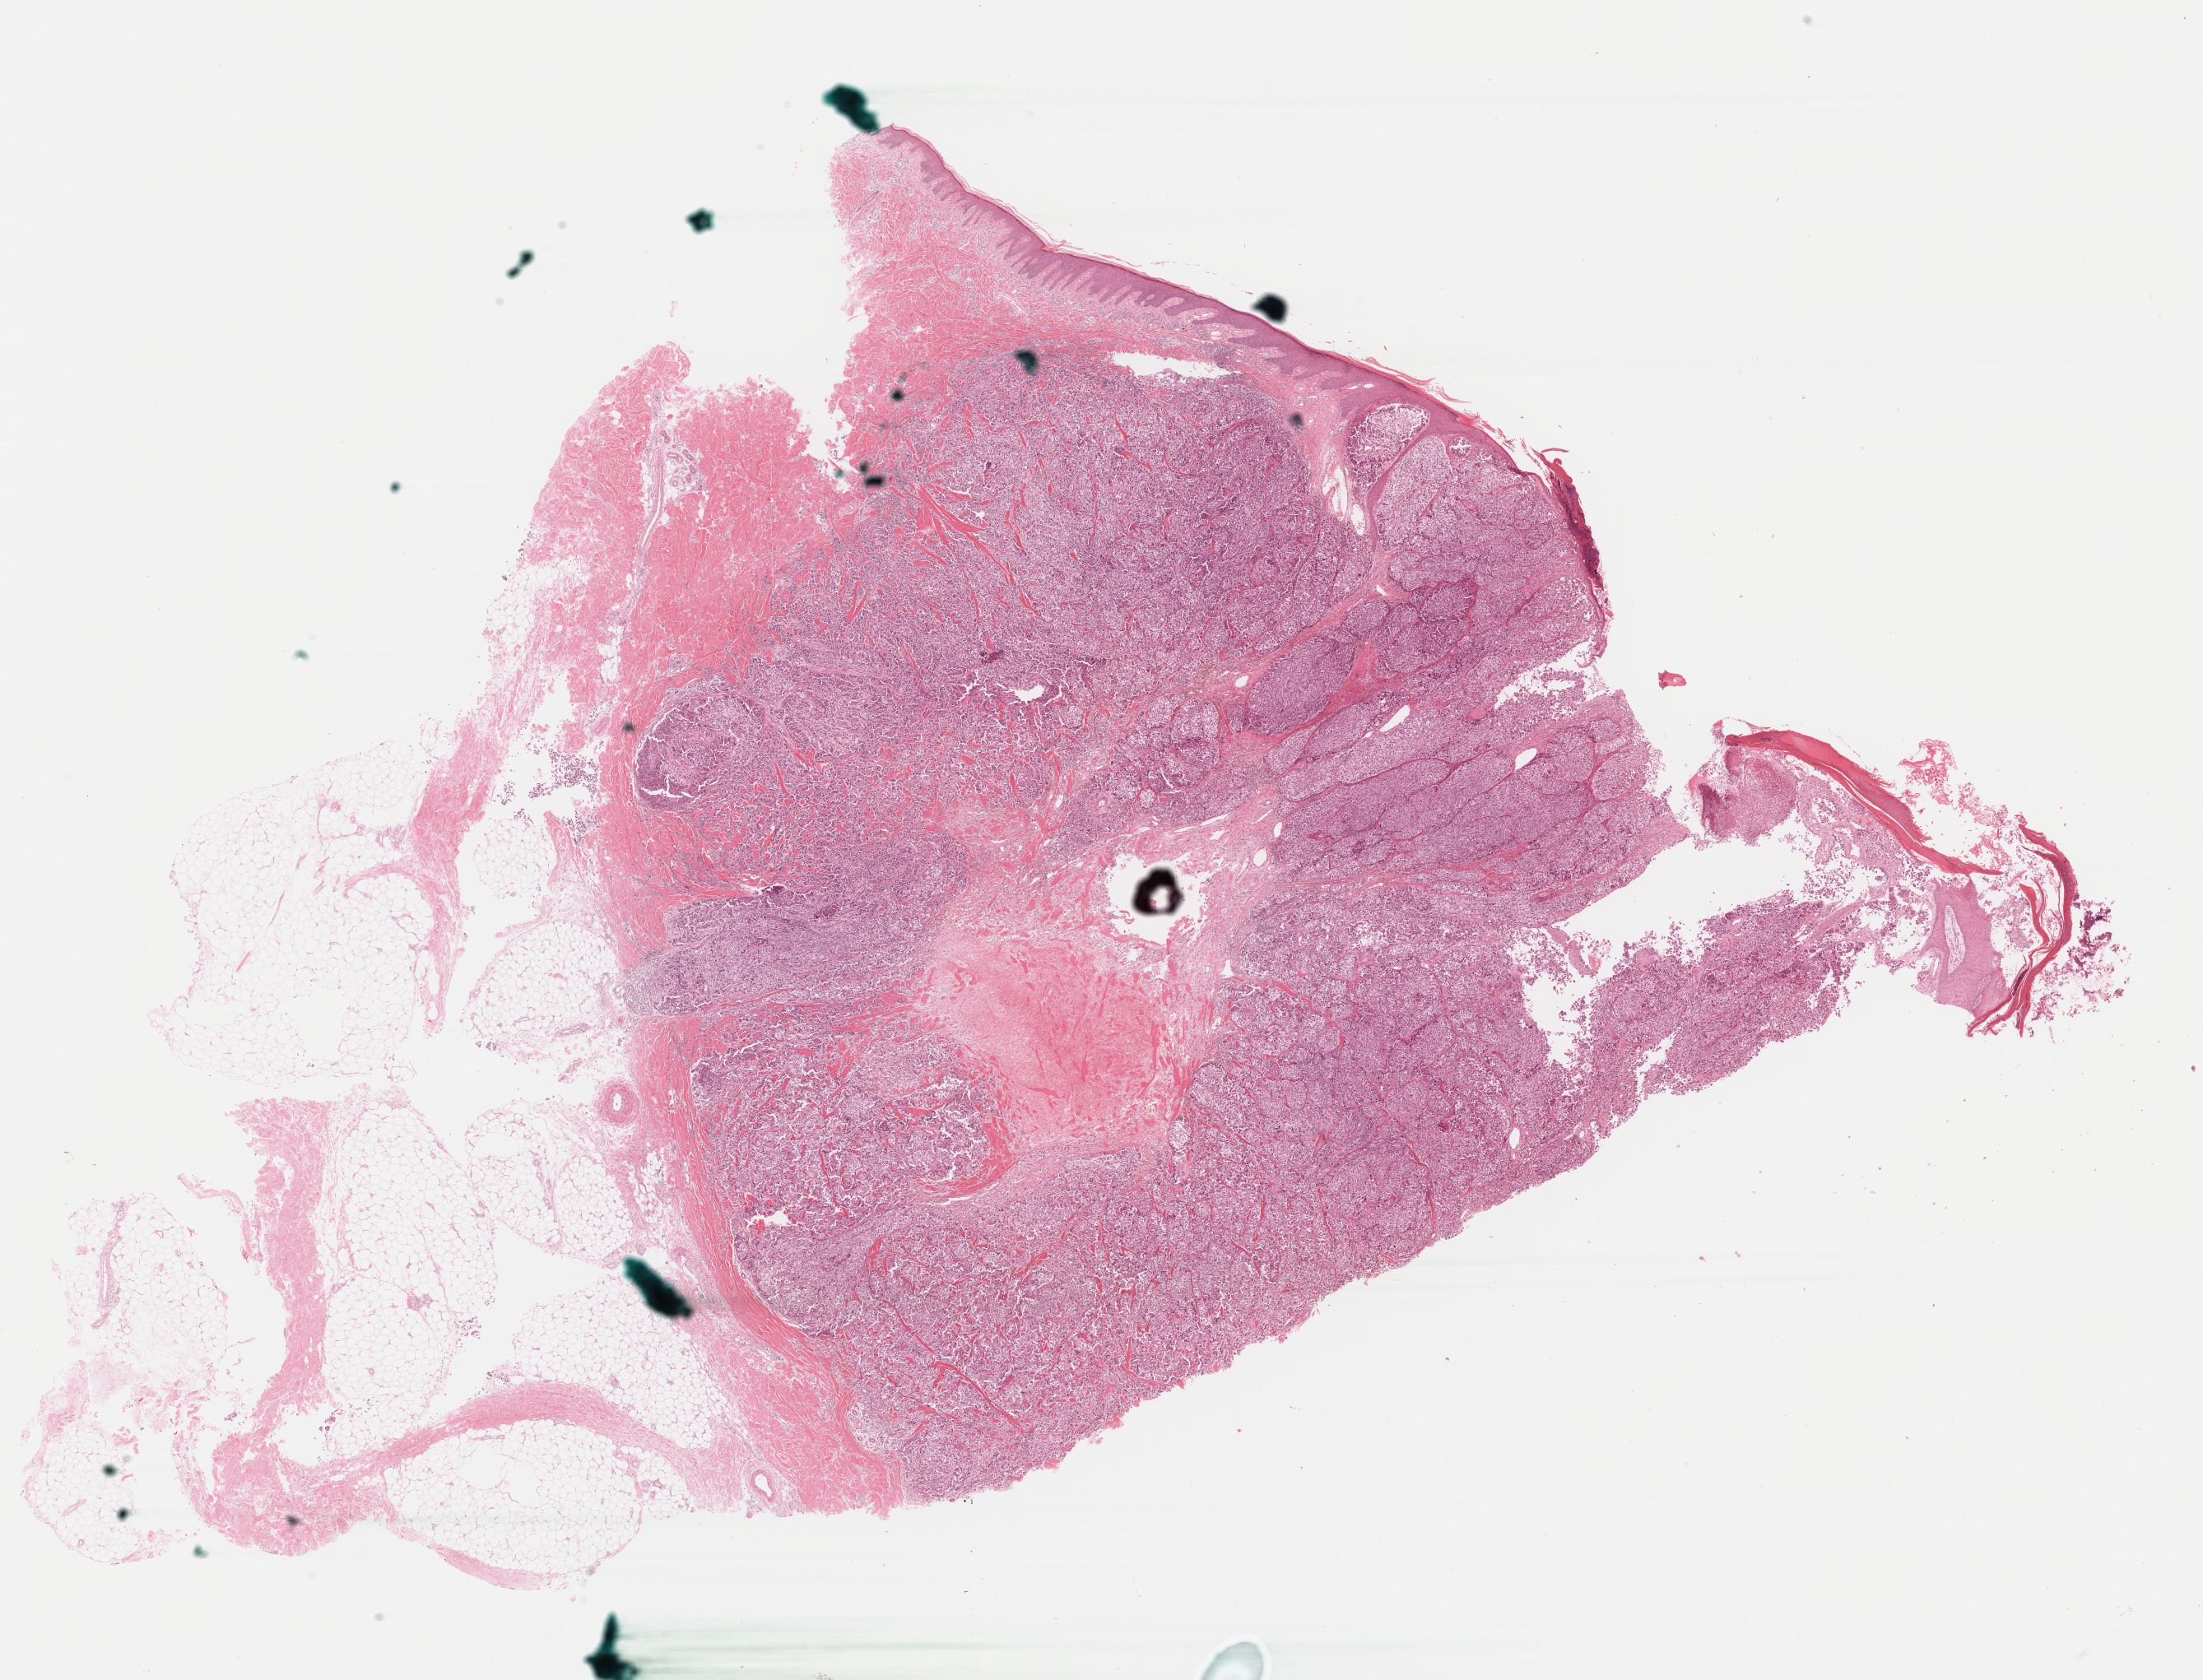
Whole-slide histology image, H&E, low-resolution overview of the scanned area, about 21.1 x 16.1 mm. Formalin-fixed paraffin-embedded (FFPE) diagnostic section. Skin, primary tumour sample. Patient: female, age at initial diagnosis 65 years.
Histologic diagnosis: Malignant melanoma, NOS.